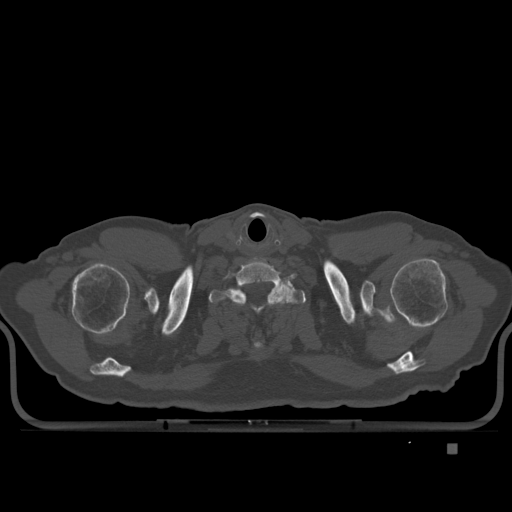
CT including the spine, one axial slice. Position 330 of 435 along the scan axis. Bone window (W 1800 / L 400 HU). 1.5 mm slice thickness. 512 × 512 image matrix, field of view 434 × 434 mm. Patient: male, 73 years. From the clinical record (not read from this slice): primary cancer: skin.
Outlined on this slice (semi-automatic segmentation, software-assisted and operator-edited):
- T1 vertebra: bounding box <210,282,305,349> (left, top, right, bottom; pixels)